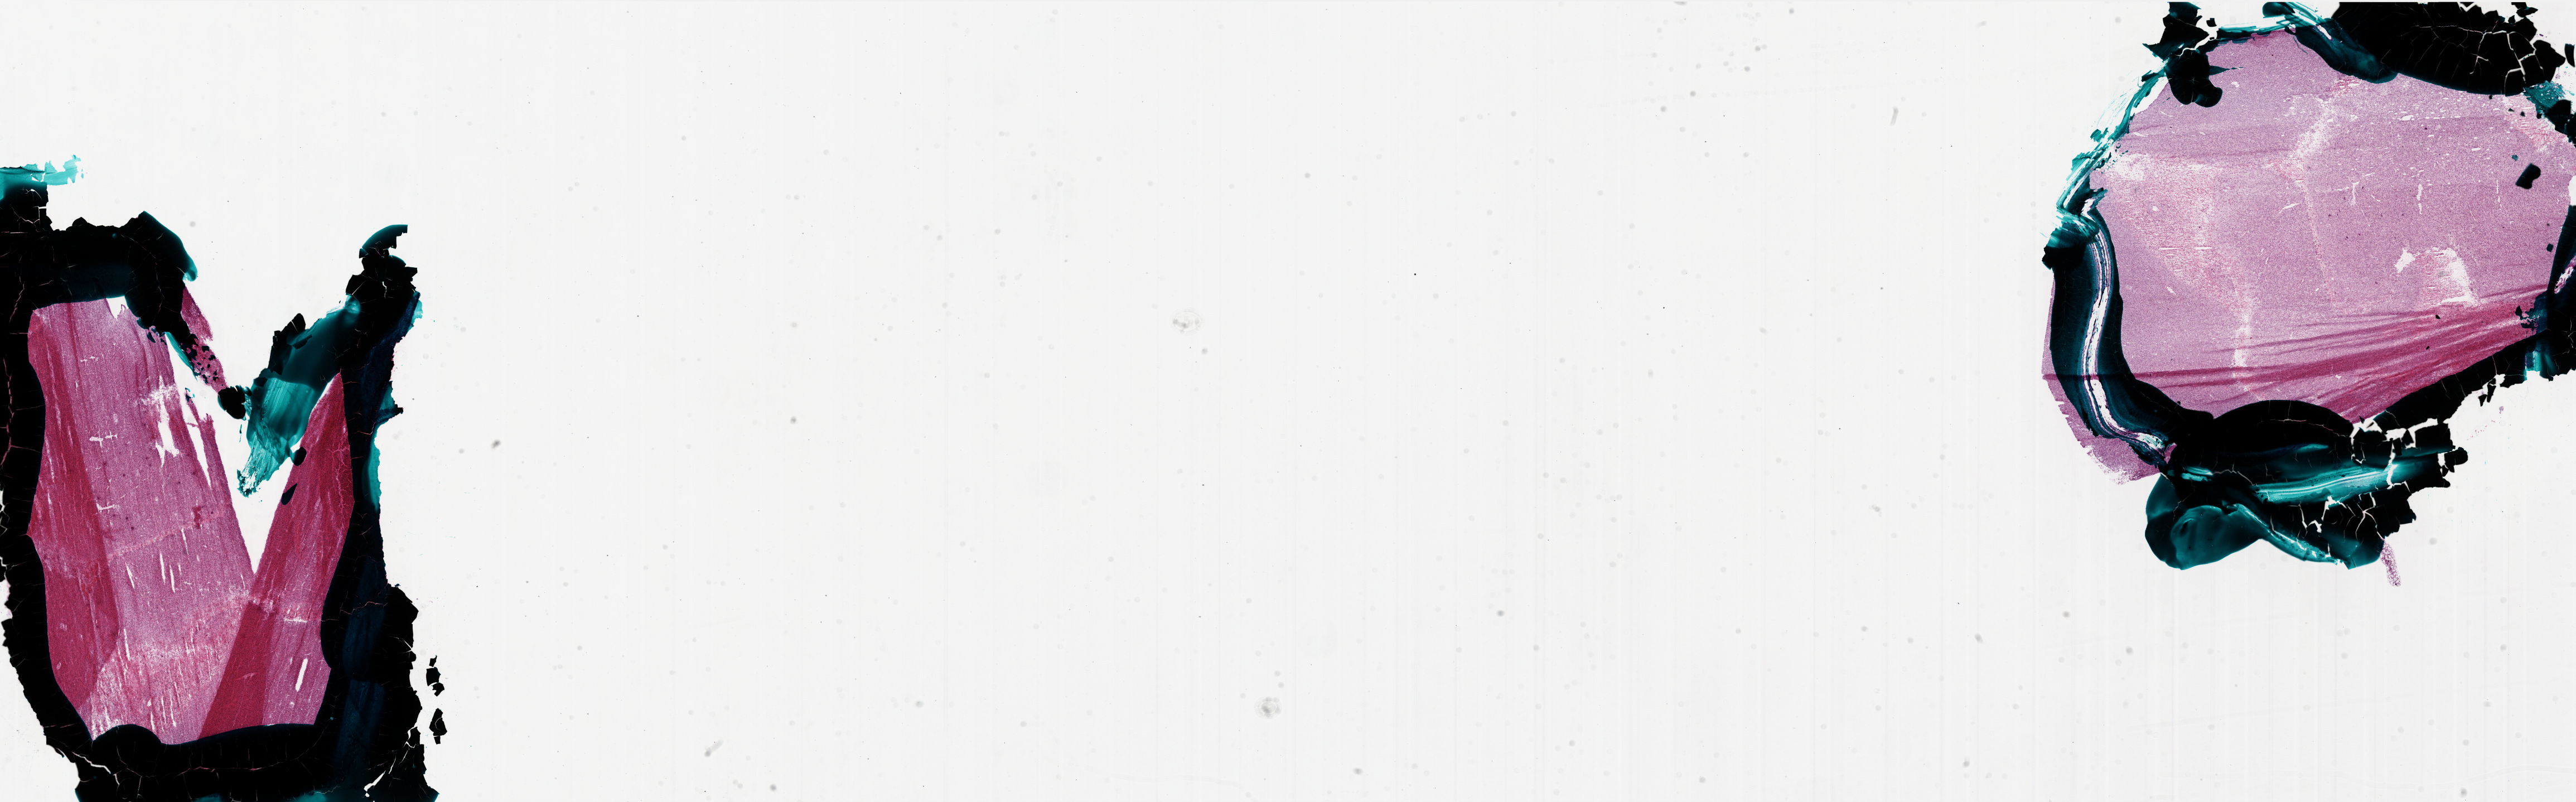
Digitized Hematoxylin and eosin (H&E) stained tissue section (whole slide) — shown as a low-resolution overview of the whole scanned area (about 37.0 x 11.5 mm, from a 20x scan); frozen section; brain, primary tumour sample. Female, age 53 years at initial diagnosis. Slide review estimates, as recorded: tumour cells 90%, tumour nuclei 100%, normal cells 0%, stromal cells 0%, necrosis 10%. Inflammatory infiltration, as recorded: lymphocyte infiltration 0%, monocyte infiltration 0%, neutrophil infiltration 0%.
• diagnosis: Glioblastoma